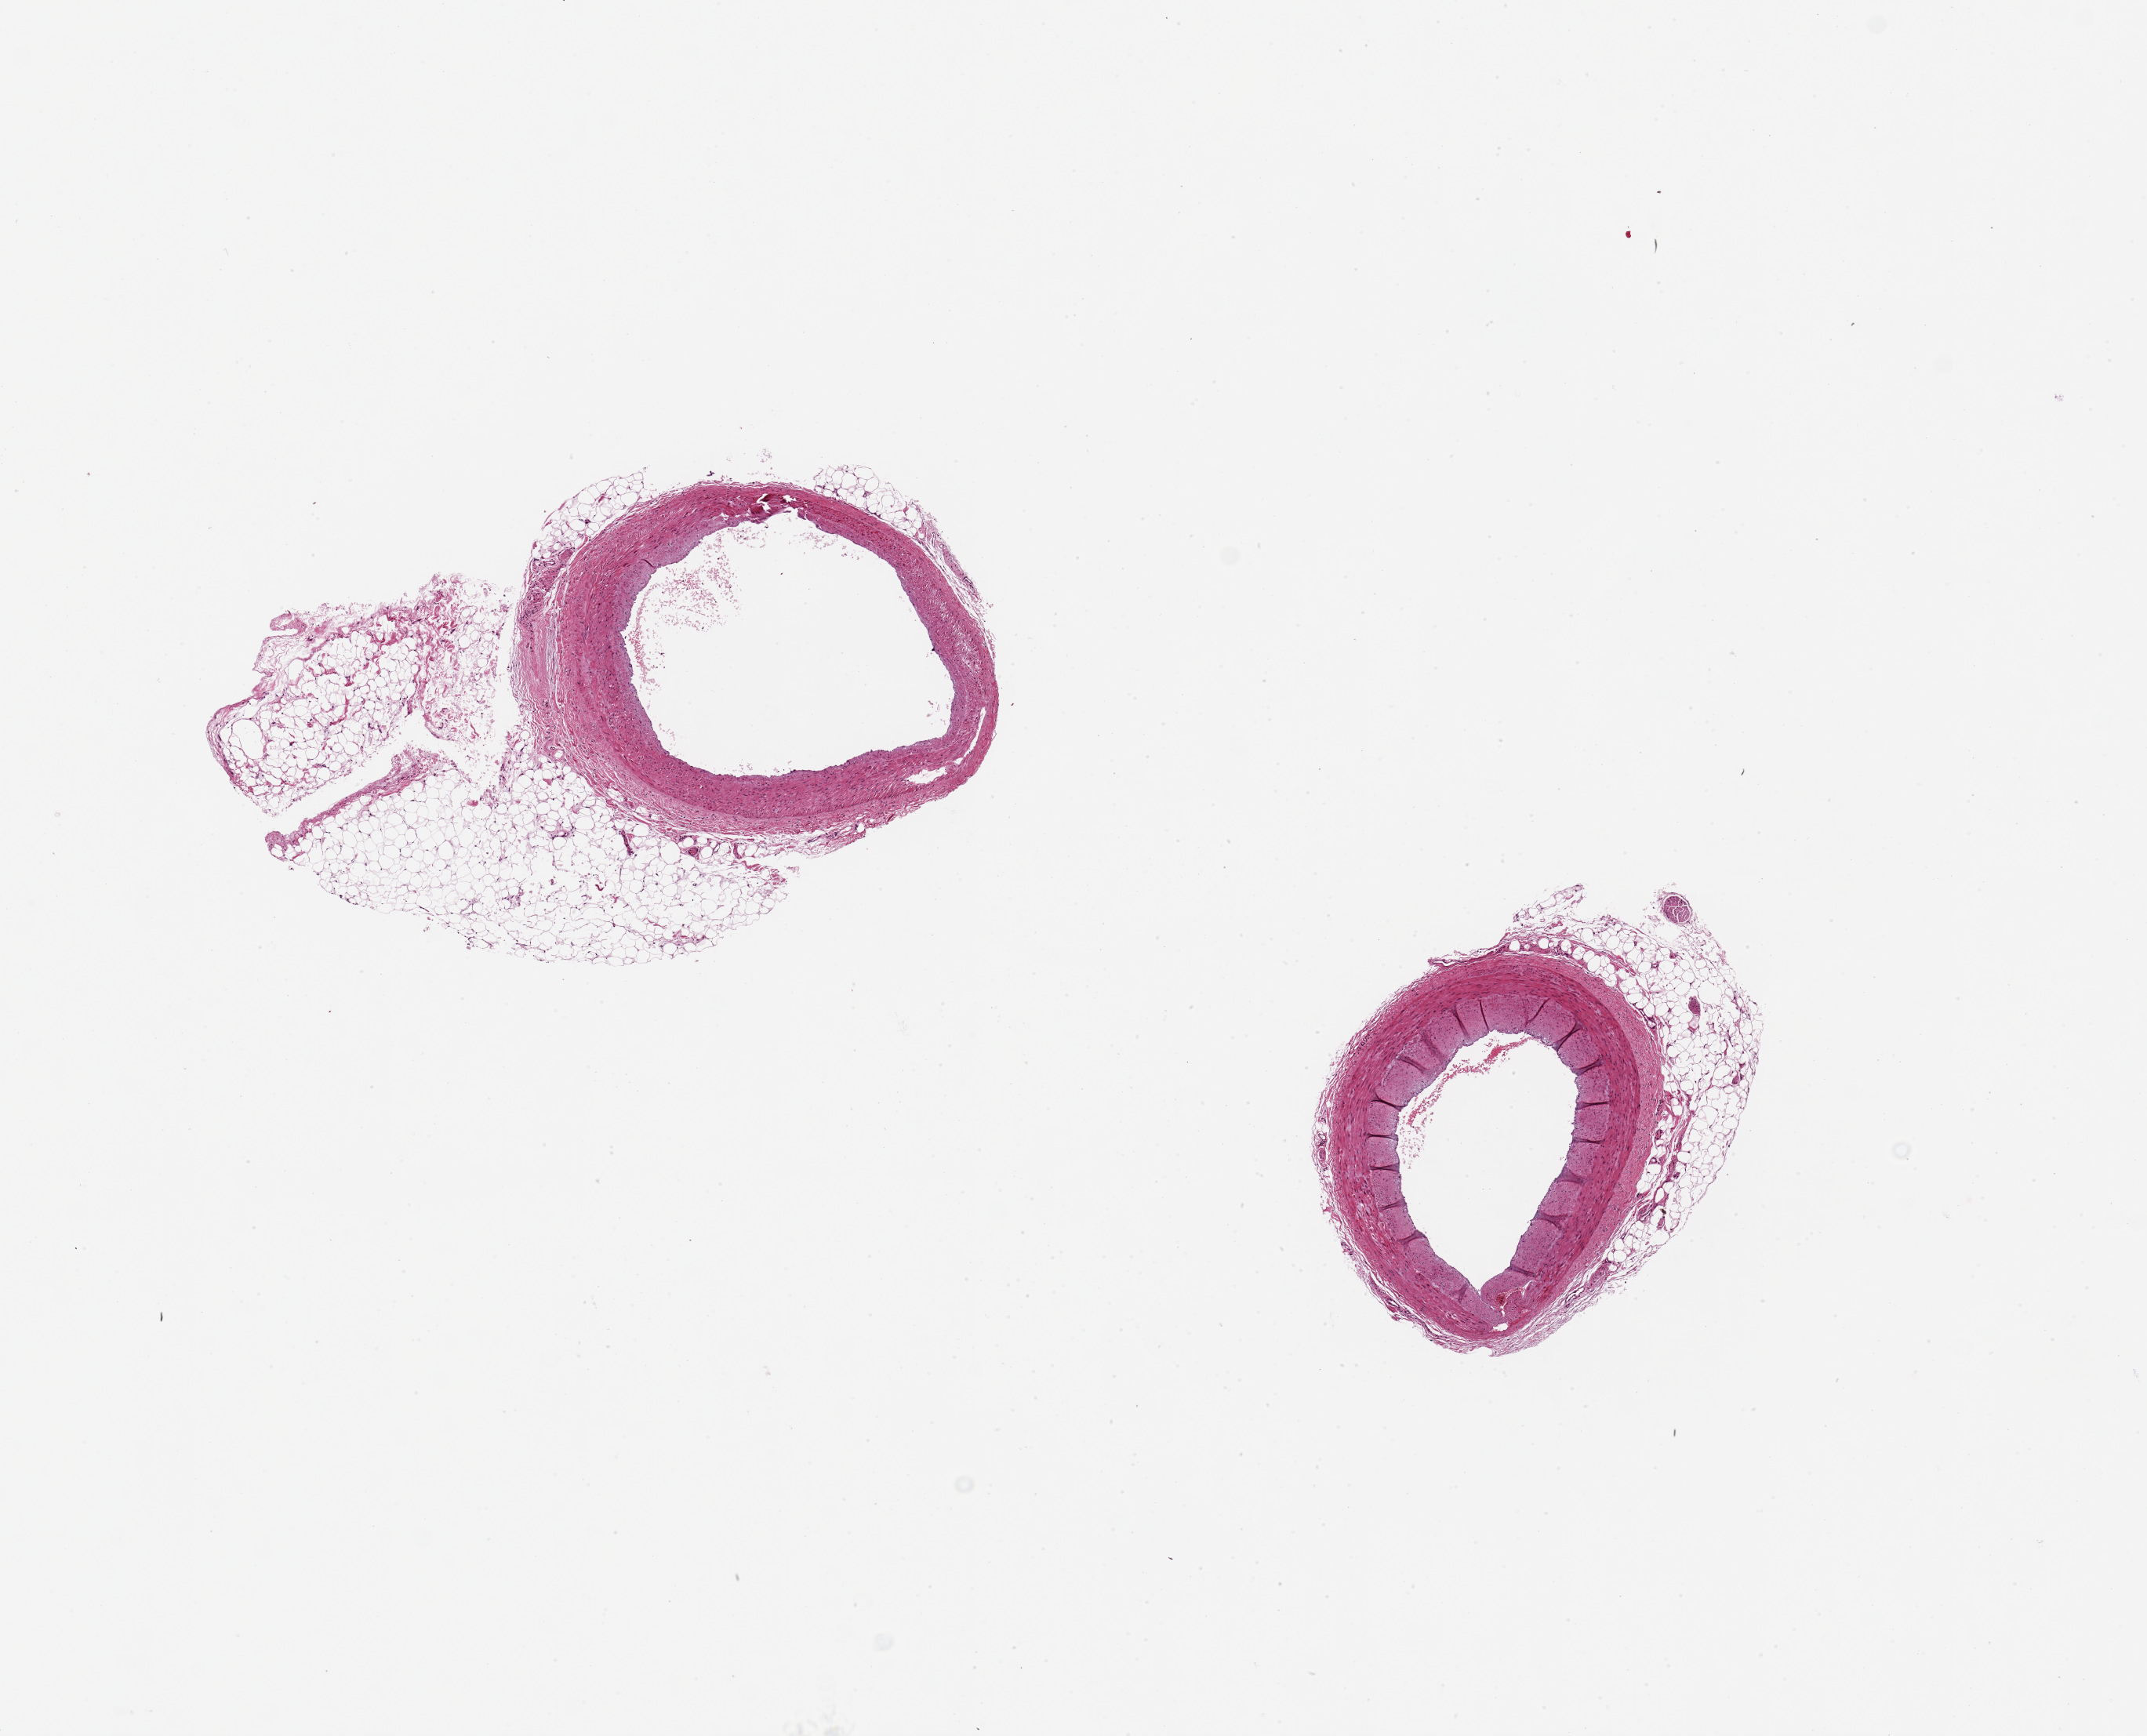
Haematoxylin and eosin whole-slide image, brightfield — whole scanned area (about 10.8 x 8.8 mm) shown as a low-resolution overview. PAXgene-fixed, paraffin-embedded tissue. Section of coronary artery (target tissue). Tissue donor sample.
Review note (as recorded): 2 pieces, 4x2.5 & 3x2mm; no plaques; ~40% surrounding adipose, up to 1 mm thick.